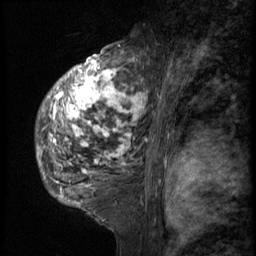
Breast MRI (dynamic contrast-enhanced), one sagittal slice. Slice 37 of 58 in the series (ordered by position). 3 images stored at this slice position (order not interpretable as contrast timing). 1.5 T. TE 4.2 ms, TR 9 ms. 256 × 256 image matrix, field of view 180 × 180 mm. Patient: female, 50 years. Case-level facts recorded for this patient, not image findings: setting: breast cancer imaged before/during neoadjuvant chemotherapy; receptor status: triple-negative.
Structures marked on this image (semi-automatically segmented with operator editing):
- analysis volume of interest (the breast-tissue region the enhancement analysis was run in; not a lesion): bounding box [x1, y1, x2, y2] px = [36, 48, 137, 214]
- tumour enhancement mask (voxels above the 140 % enhancement threshold inside the analysis volume of interest): [38, 54, 137, 204]